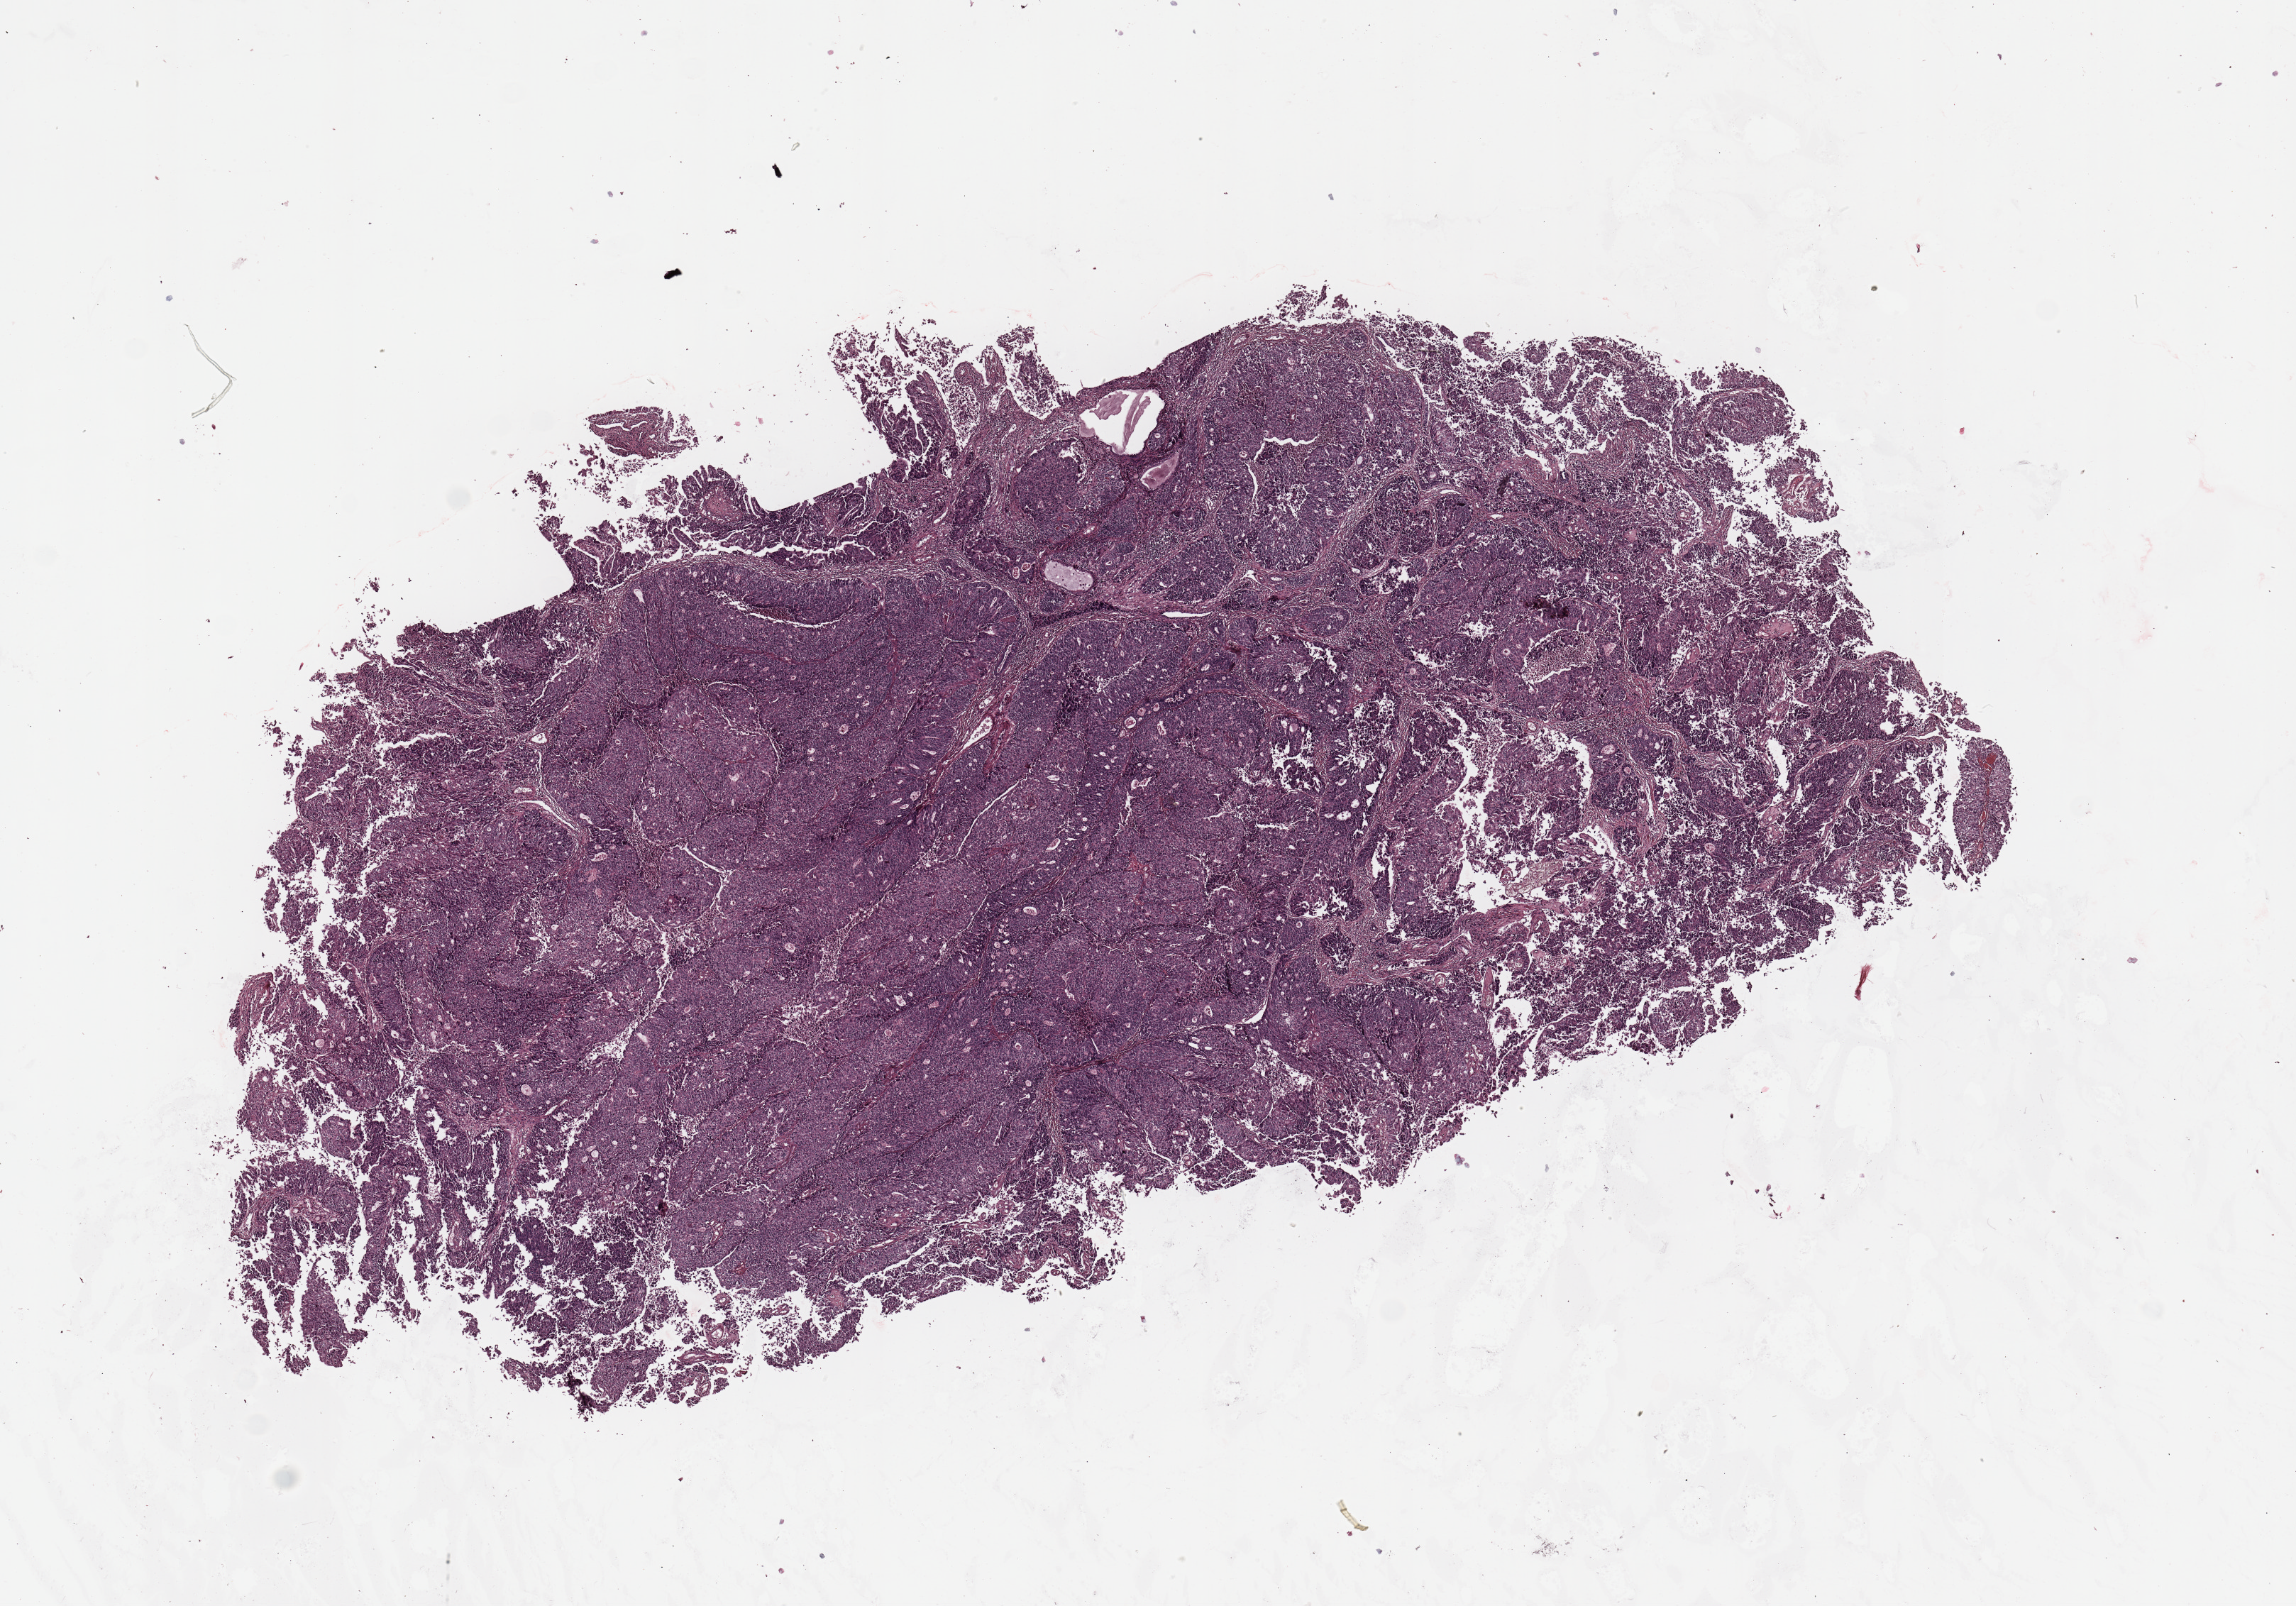
Whole-slide histology image, Hematoxylin and eosin (H&E) stained, shown as a low-resolution overview of the whole scanned area (about 12.8 x 8.9 mm, acquisition: 20x scan); uterus, tumour tissue. Female, 75 y/o. Histologic grade: G3 (poorly differentiated).
AJCC pathologic stage: I. Histologic diagnosis: Endometrioid adenocarcinoma, NOS.